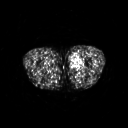
FDG PET of an extremity soft-tissue mass (from a PET/CT study), one axial slice; 3.27 mm slice thickness; 128 × 128 image matrix, field of view 500 × 500 mm. Patient: male, 29 years. From the clinical record (not read from this slice): histological type: mixoid liposarcoma; grade: low; site of the primary tumour: left thigh.
Annotated regions visible in this slice (expert contour drawn on MRI and transferred to this co-registered scan by the dataset authors):
- gross tumour volume (mass): bounding box [x1, y1, x2, y2] px = [70, 53, 82, 70]